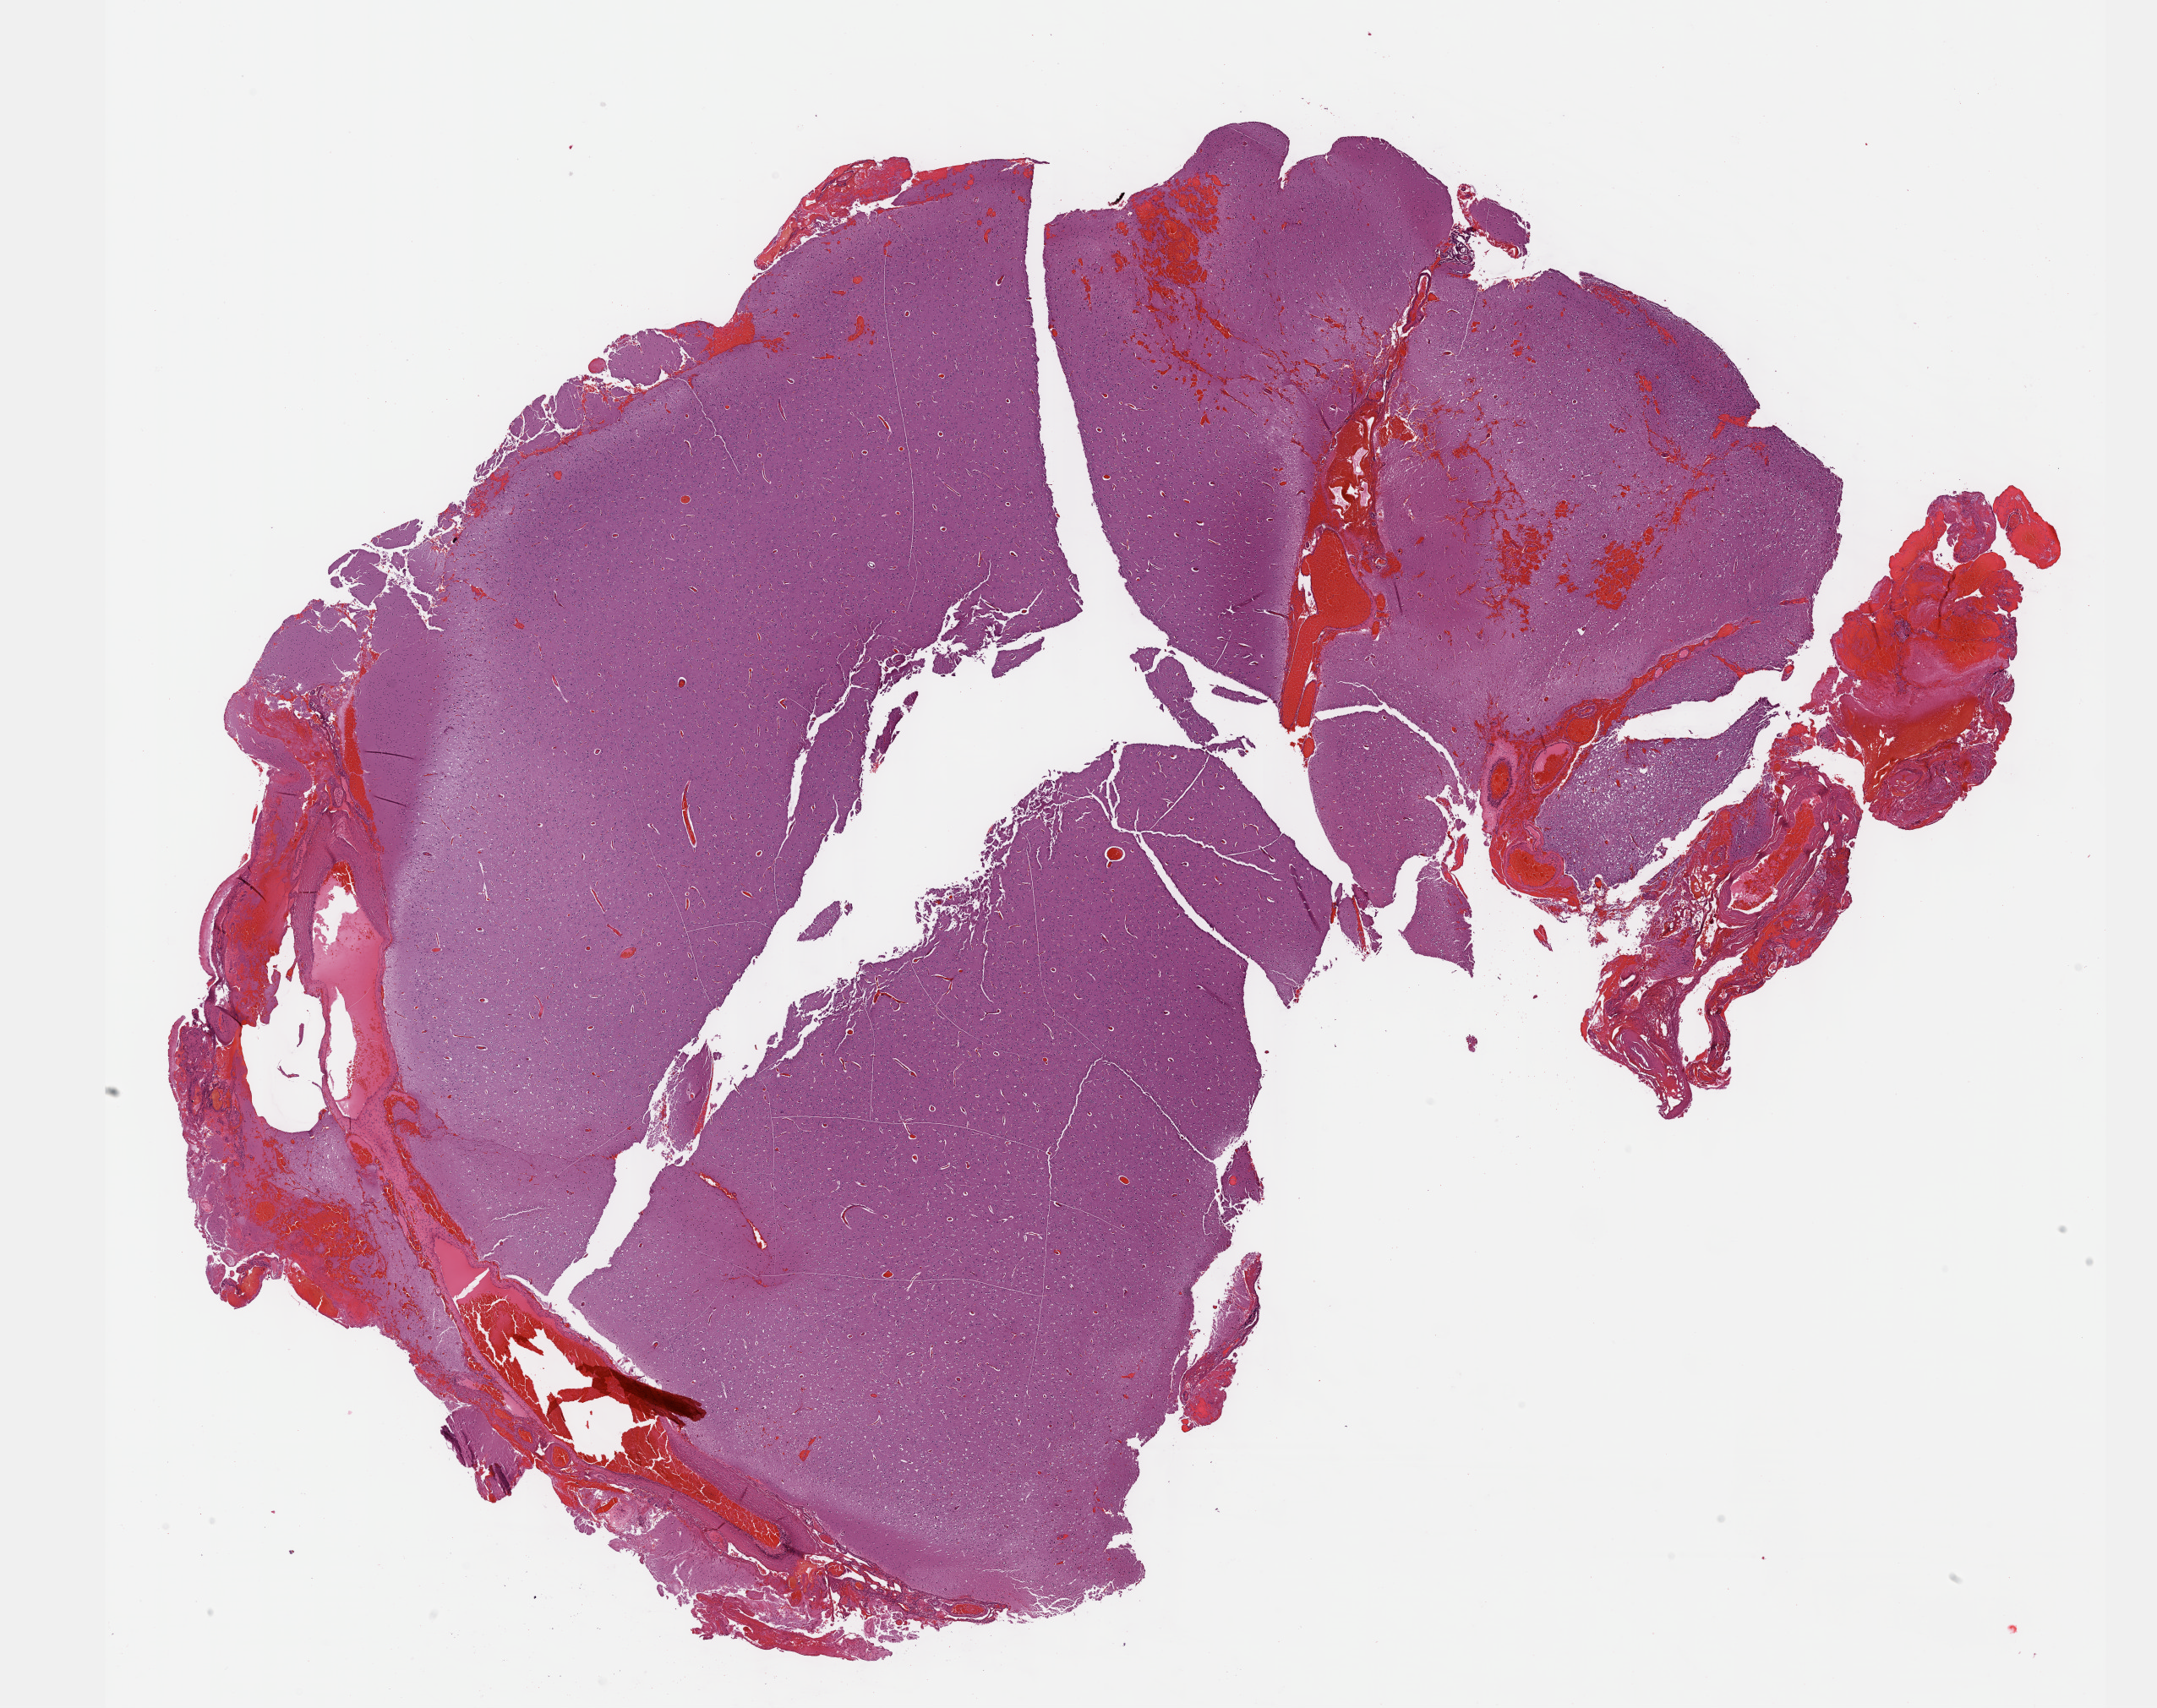
H&E whole-slide image — low-resolution overview of the scanned area, about 20.6 x 16.3 mm (from a 40x scan). FFPE section. Sample: primary tumour, brain. Male patient; age at initial diagnosis 31 years. Histologic grade: G3 (poorly differentiated).
Laterality: right. Diagnosis: Mixed glioma (cerebrum).